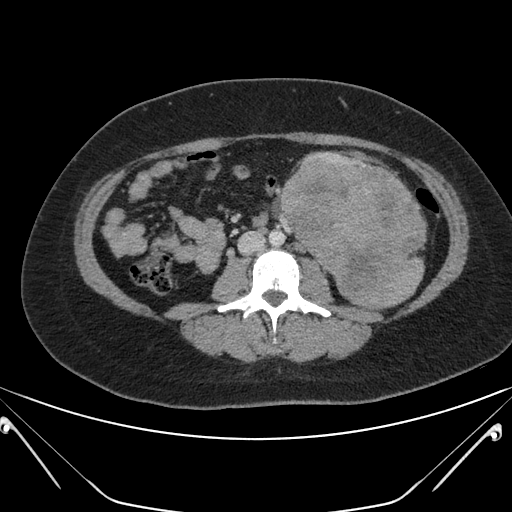
Contrast-enhanced abdominal CT, one axial slice. Slice 90 of 168 in the series (ordered by position). Intravenous contrast given. Soft-tissue window (W 400 / L 40 HU). 512 × 512 image matrix. Patient: female, 26 years. Case-level facts recorded for this patient, not image findings: diagnosis: adrenocortical carcinoma; tumour side: left adrenal; tumour size at pathology: 28 cm; Ki-67 index: 20 %; stage (as recorded): 2.
Structures marked on this image (semi-automatic segmentation, software-assisted and operator-edited):
- mass: box from (x=282, y=154) to (x=425, y=305) px